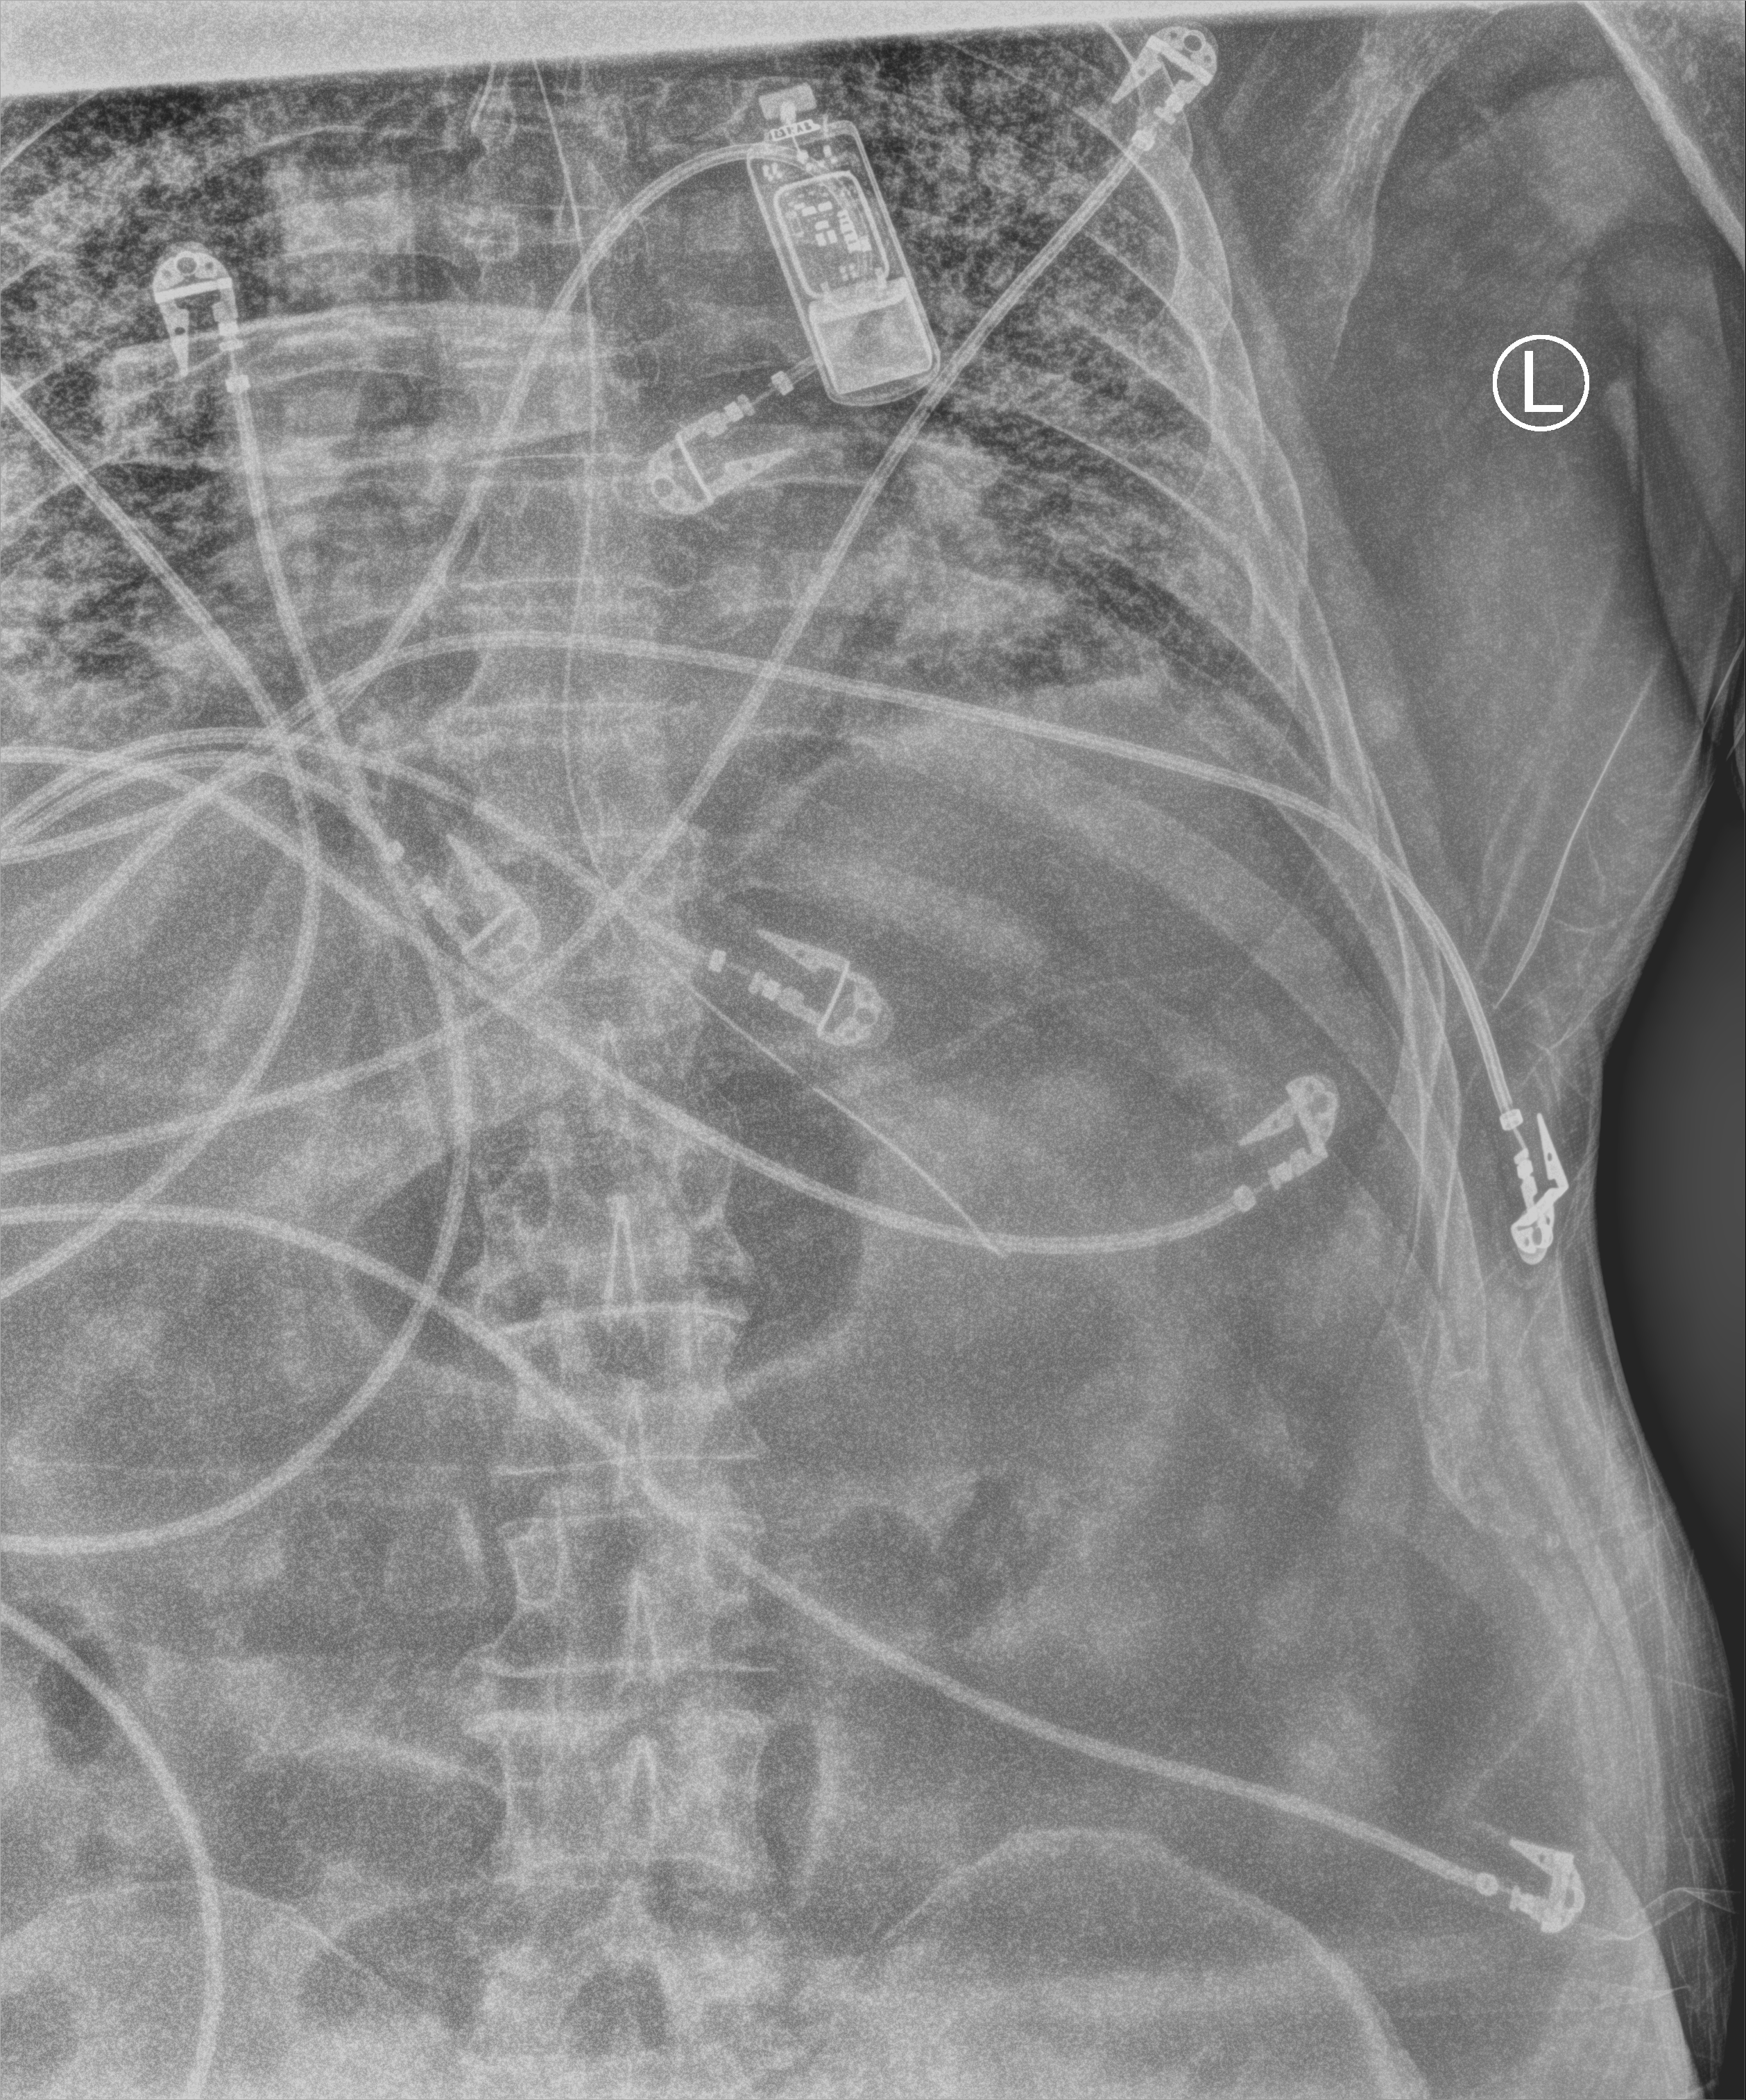
Bedside chest radiograph (computed radiography), anteroposterior (AP) projection. Patient hospitalised with COVID-19; male, aged 60–74 years.
From the hospital-stay record, not from the radiograph (when in the stay this image was taken is not recorded):
- hypertension (admission record): yes